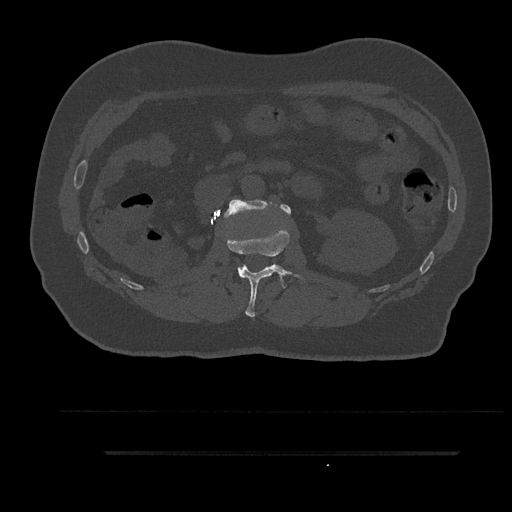
CT including the spine, one axial slice; slice 158 of 797 in the series (ordered by position); bone window (W 1800 / L 400 HU); 0.5 mm slice thickness; 512 × 512 image matrix, field of view 432 × 432 mm. Male patient, age 63 years. From the clinical record (not read from this slice): primary cancer: renal; vertebrae with lytic lesions (as recorded): T8.
Outlined on this slice (semi-automatically segmented with operator editing):
- L1 vertebra: bounding box (x1, y1, x2, y2) in pixels: (226, 228, 300, 317)
- L2 vertebra: (224, 199, 291, 218)